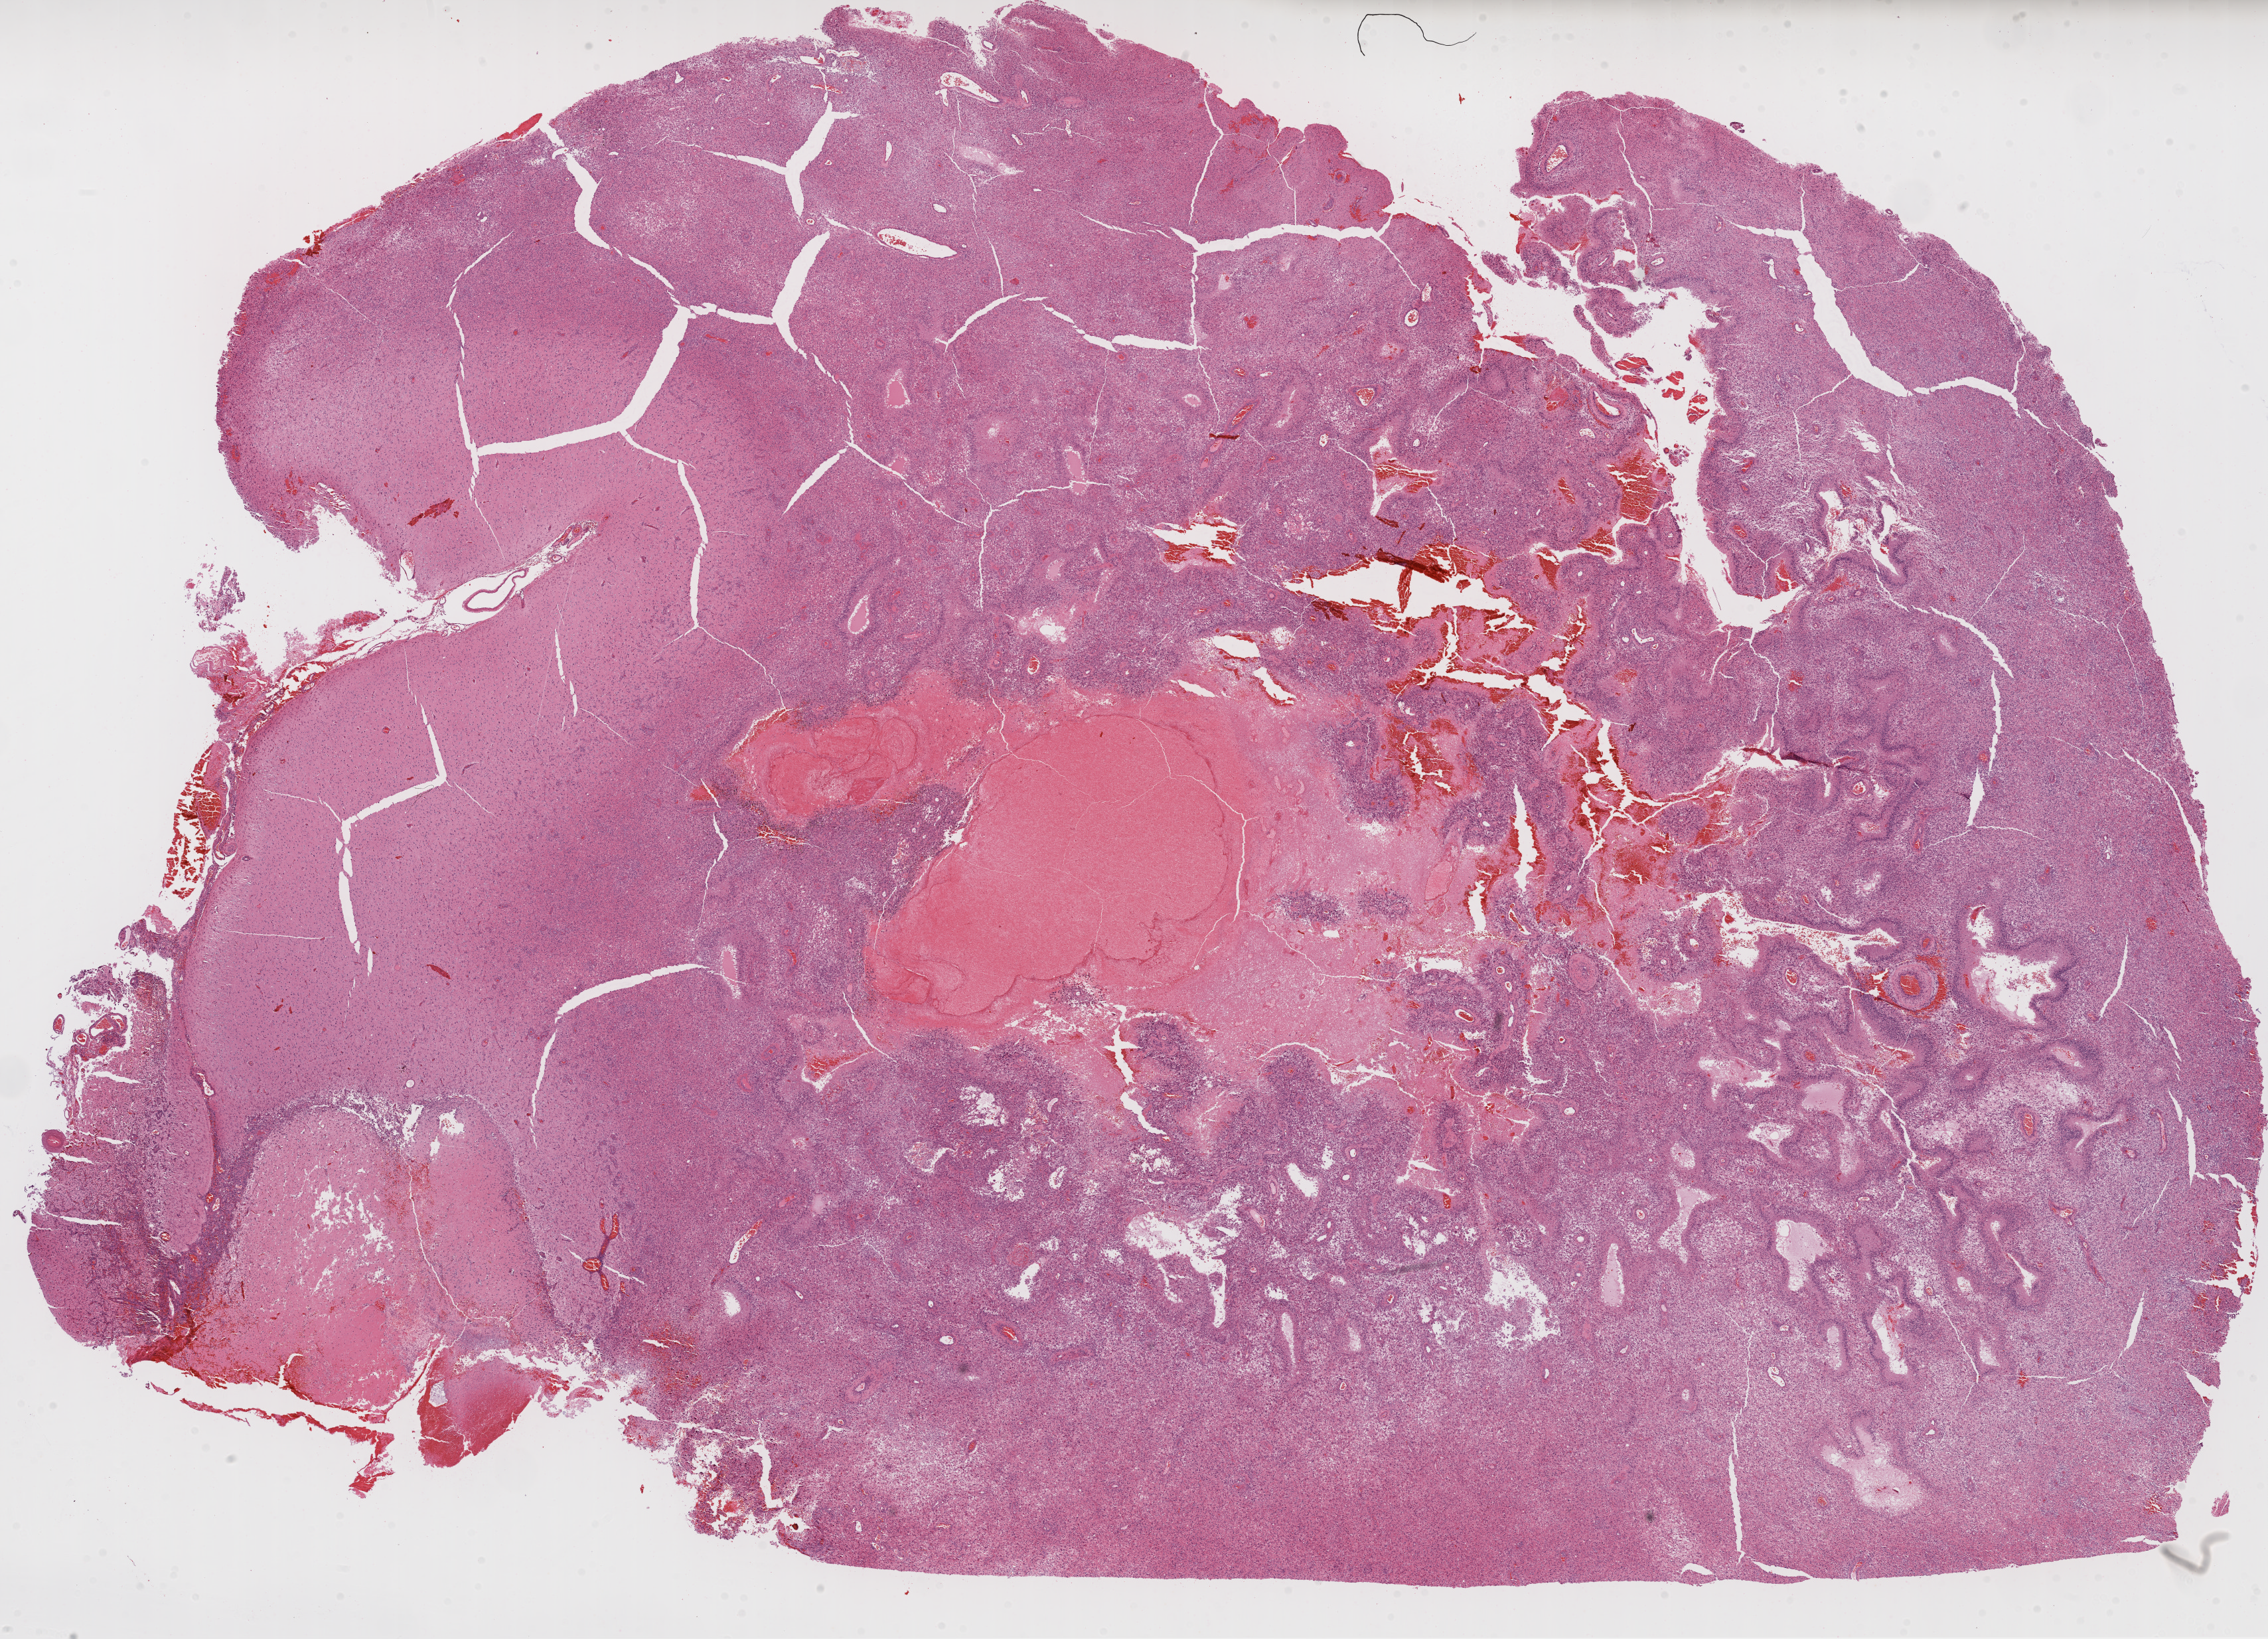
Whole-slide histology image, Hematoxylin and eosin (H&E) stained — a low-resolution overview of the entire scanned area, about 27.6 x 19.9 mm (slide scanned at 20x), formalin-fixed paraffin-embedded (FFPE) diagnostic section, brain, primary tumour sample. Male, age 66 years at initial diagnosis.
* histologic diagnosis: Glioblastoma